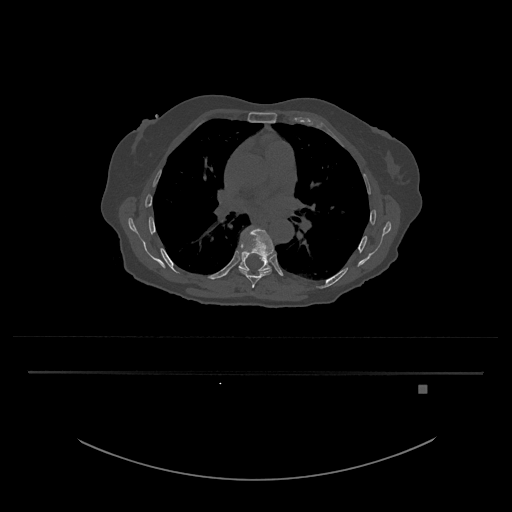
CT including the spine, one axial slice. Position 786 of 797 along the scan axis. 120 kVp. Bone window (W 1800 / L 400 HU). 0.5 mm slice thickness. 512 × 512 image matrix, field of view 500 × 500 mm. Female patient, age 57 years. From the clinical record (not read from this slice): primary cancer: cervical.
Outlined on this slice (semi-automatic segmentation, software-assisted and operator-edited):
- T8 vertebra: bounding box (x1, y1, x2, y2) in pixels: (238, 225, 274, 288)
- T9 vertebra: (236, 243, 271, 272)